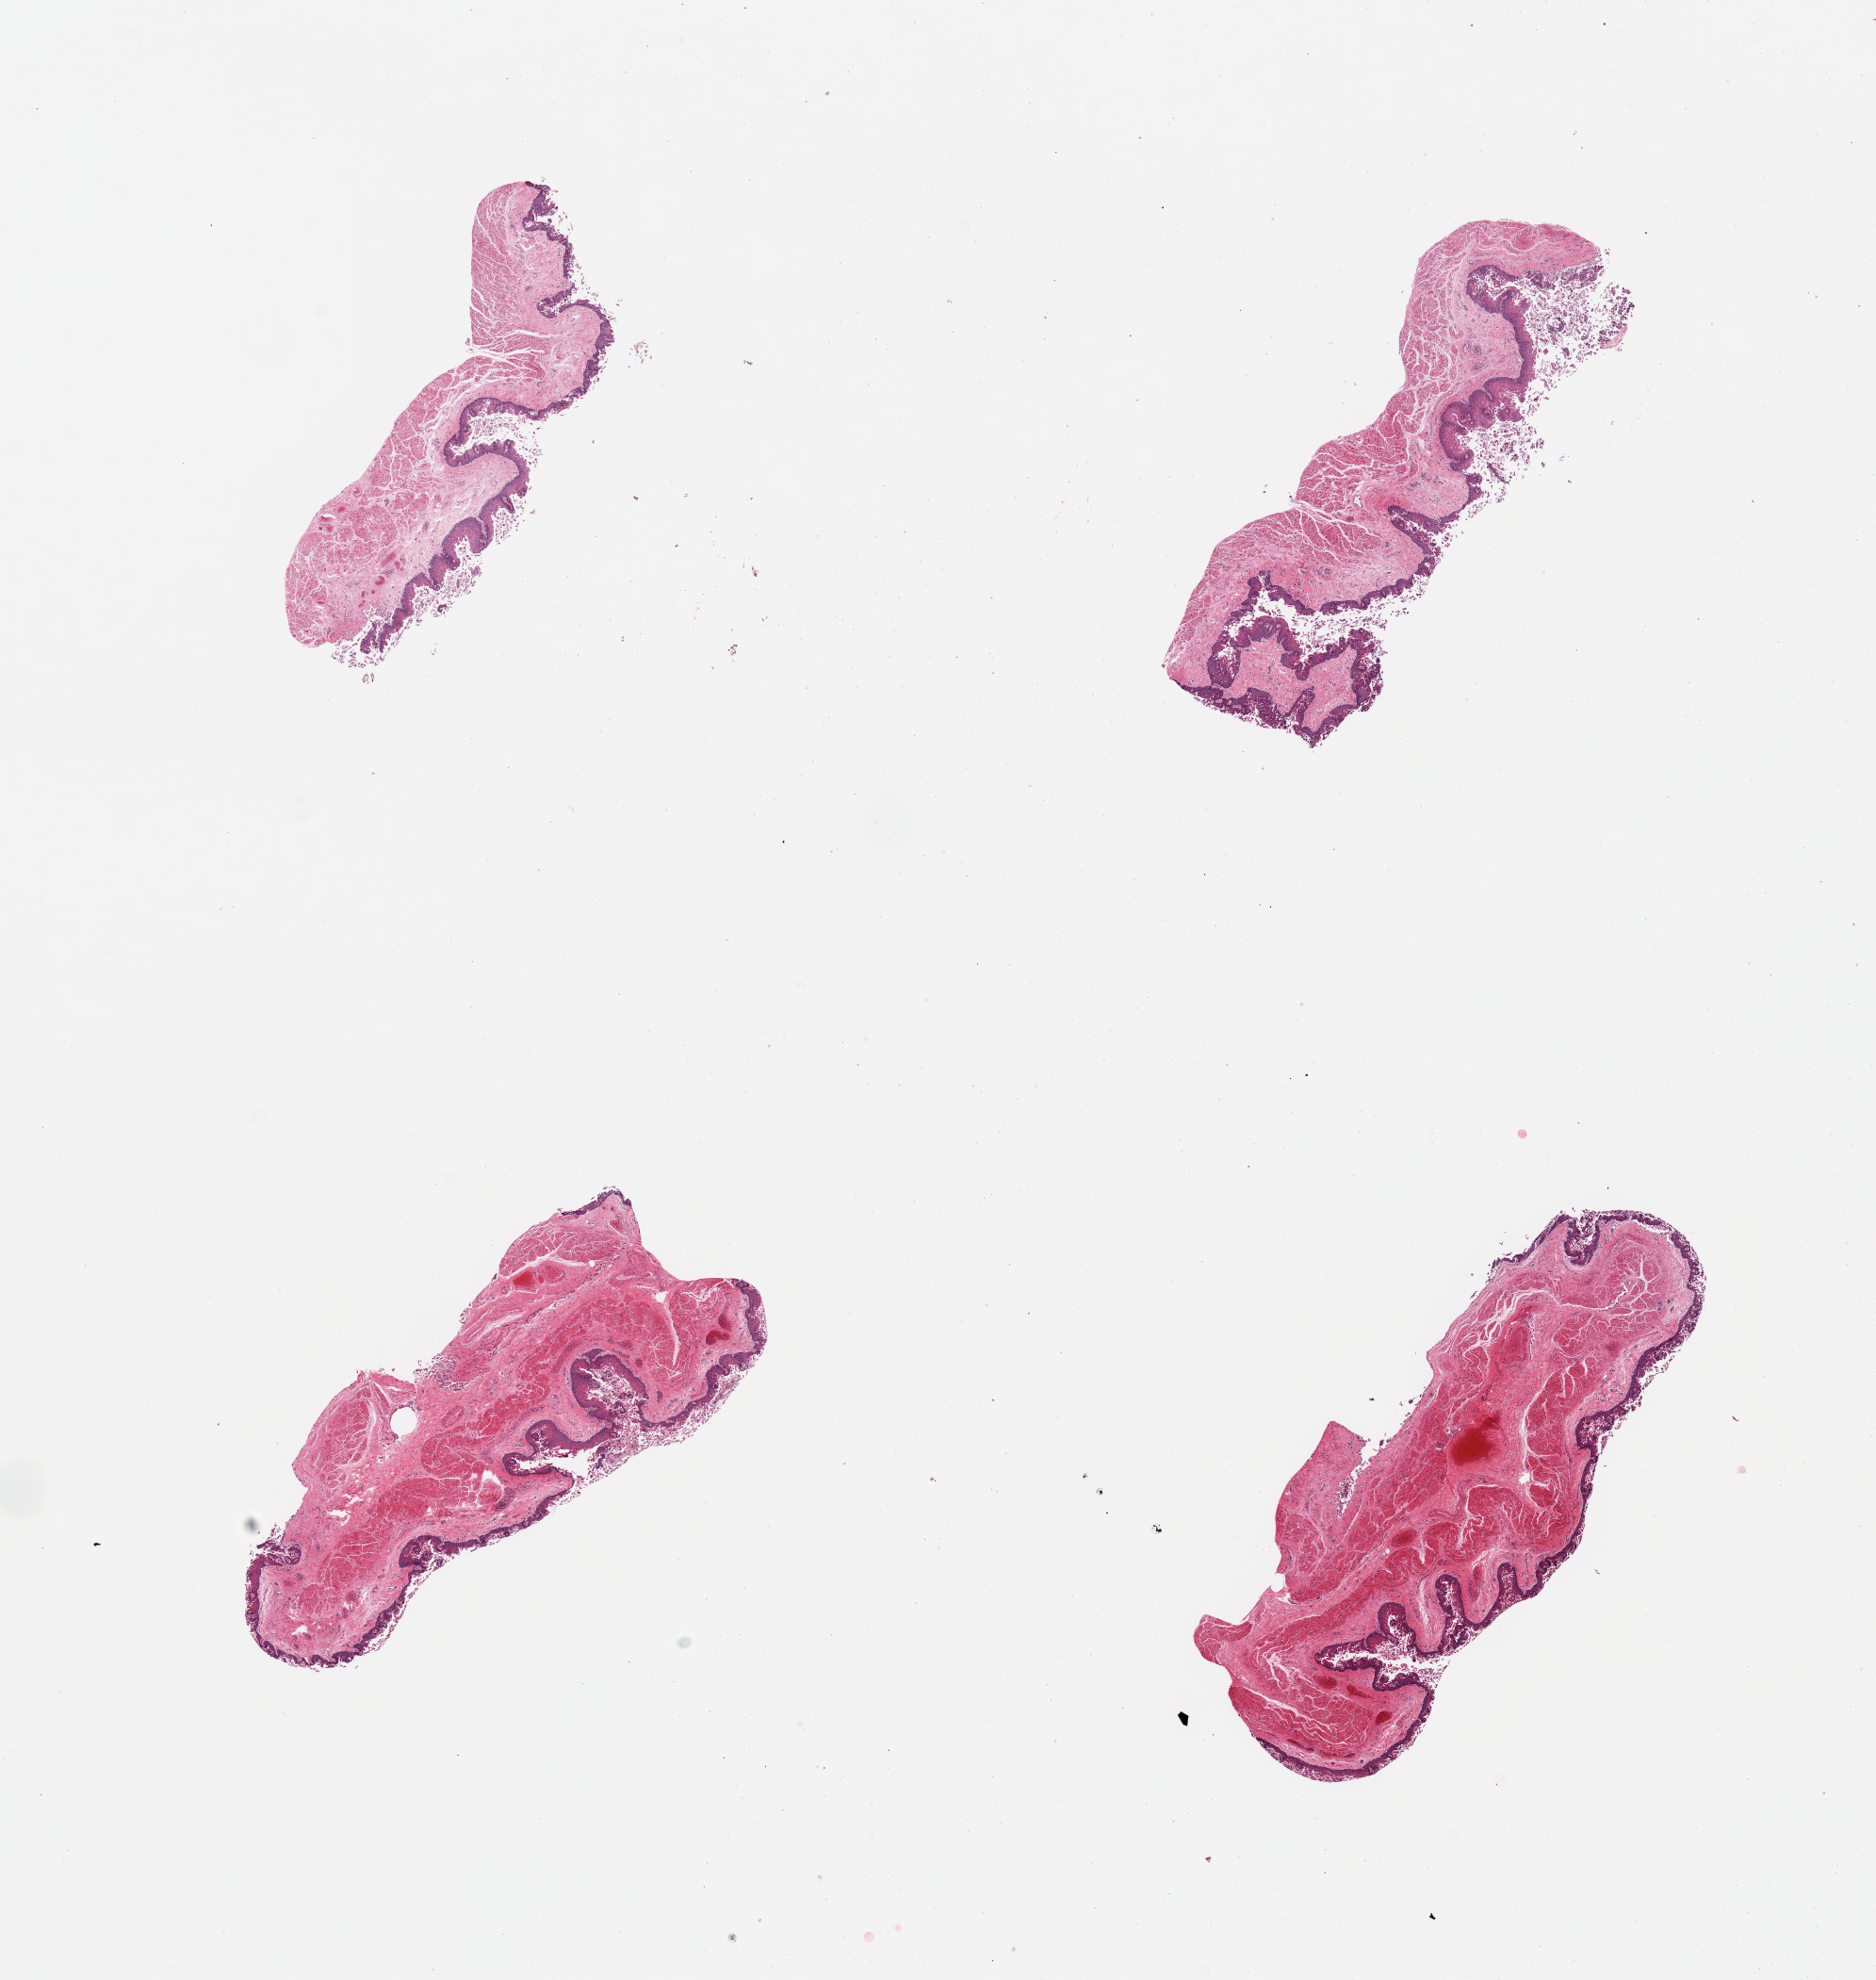
Whole-slide image, haematoxylin and eosin stain — whole scanned area (about 15.8 x 16.6 mm) shown as a low-resolution overview. PAXgene-fixed paraffin-embedded (PFPE) section. Section of esophageal mucous membrane (target tissue). Tissue donor sample. Donor: female.
Review note (as recorded): 4 pieces, mucosa partly sloughed.